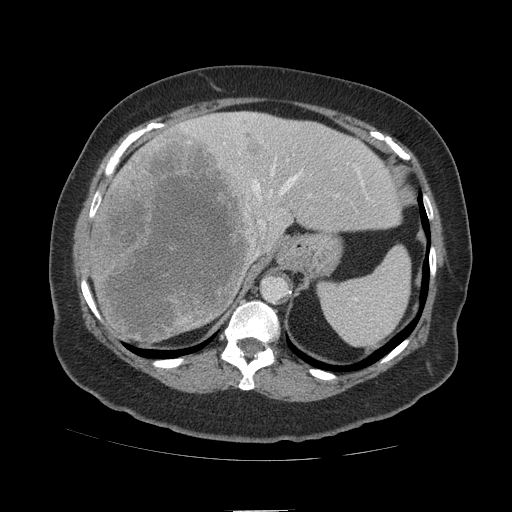
Contrast-enhanced abdominal CT (liver protocol), one axial slice. Slice 80 of 109 in the series (ordered by position). Soft-tissue window (W 400 / L 40 HU). 2.5 mm slice thickness. 512 × 512 image matrix, field of view 420 × 420 mm. Case-level facts recorded for this patient, not image findings: diagnosis: hepatocellular carcinoma (patient treated with transarterial chemoembolisation; whether this scan precedes or follows treatment is not stated here); TNM stage (as recorded): Stage-IVB.
Structures marked on this image (semi-automatic segmentation, software-assisted and operator-edited):
- liver parenchyma outside the tumour (the mass and vessels are separate outlines, so this box may not span the whole liver): bounding box <84,112,400,340> (left, top, right, bottom; pixels)
- mass: <91,127,270,342>
- liver vessels: <96,114,364,209>